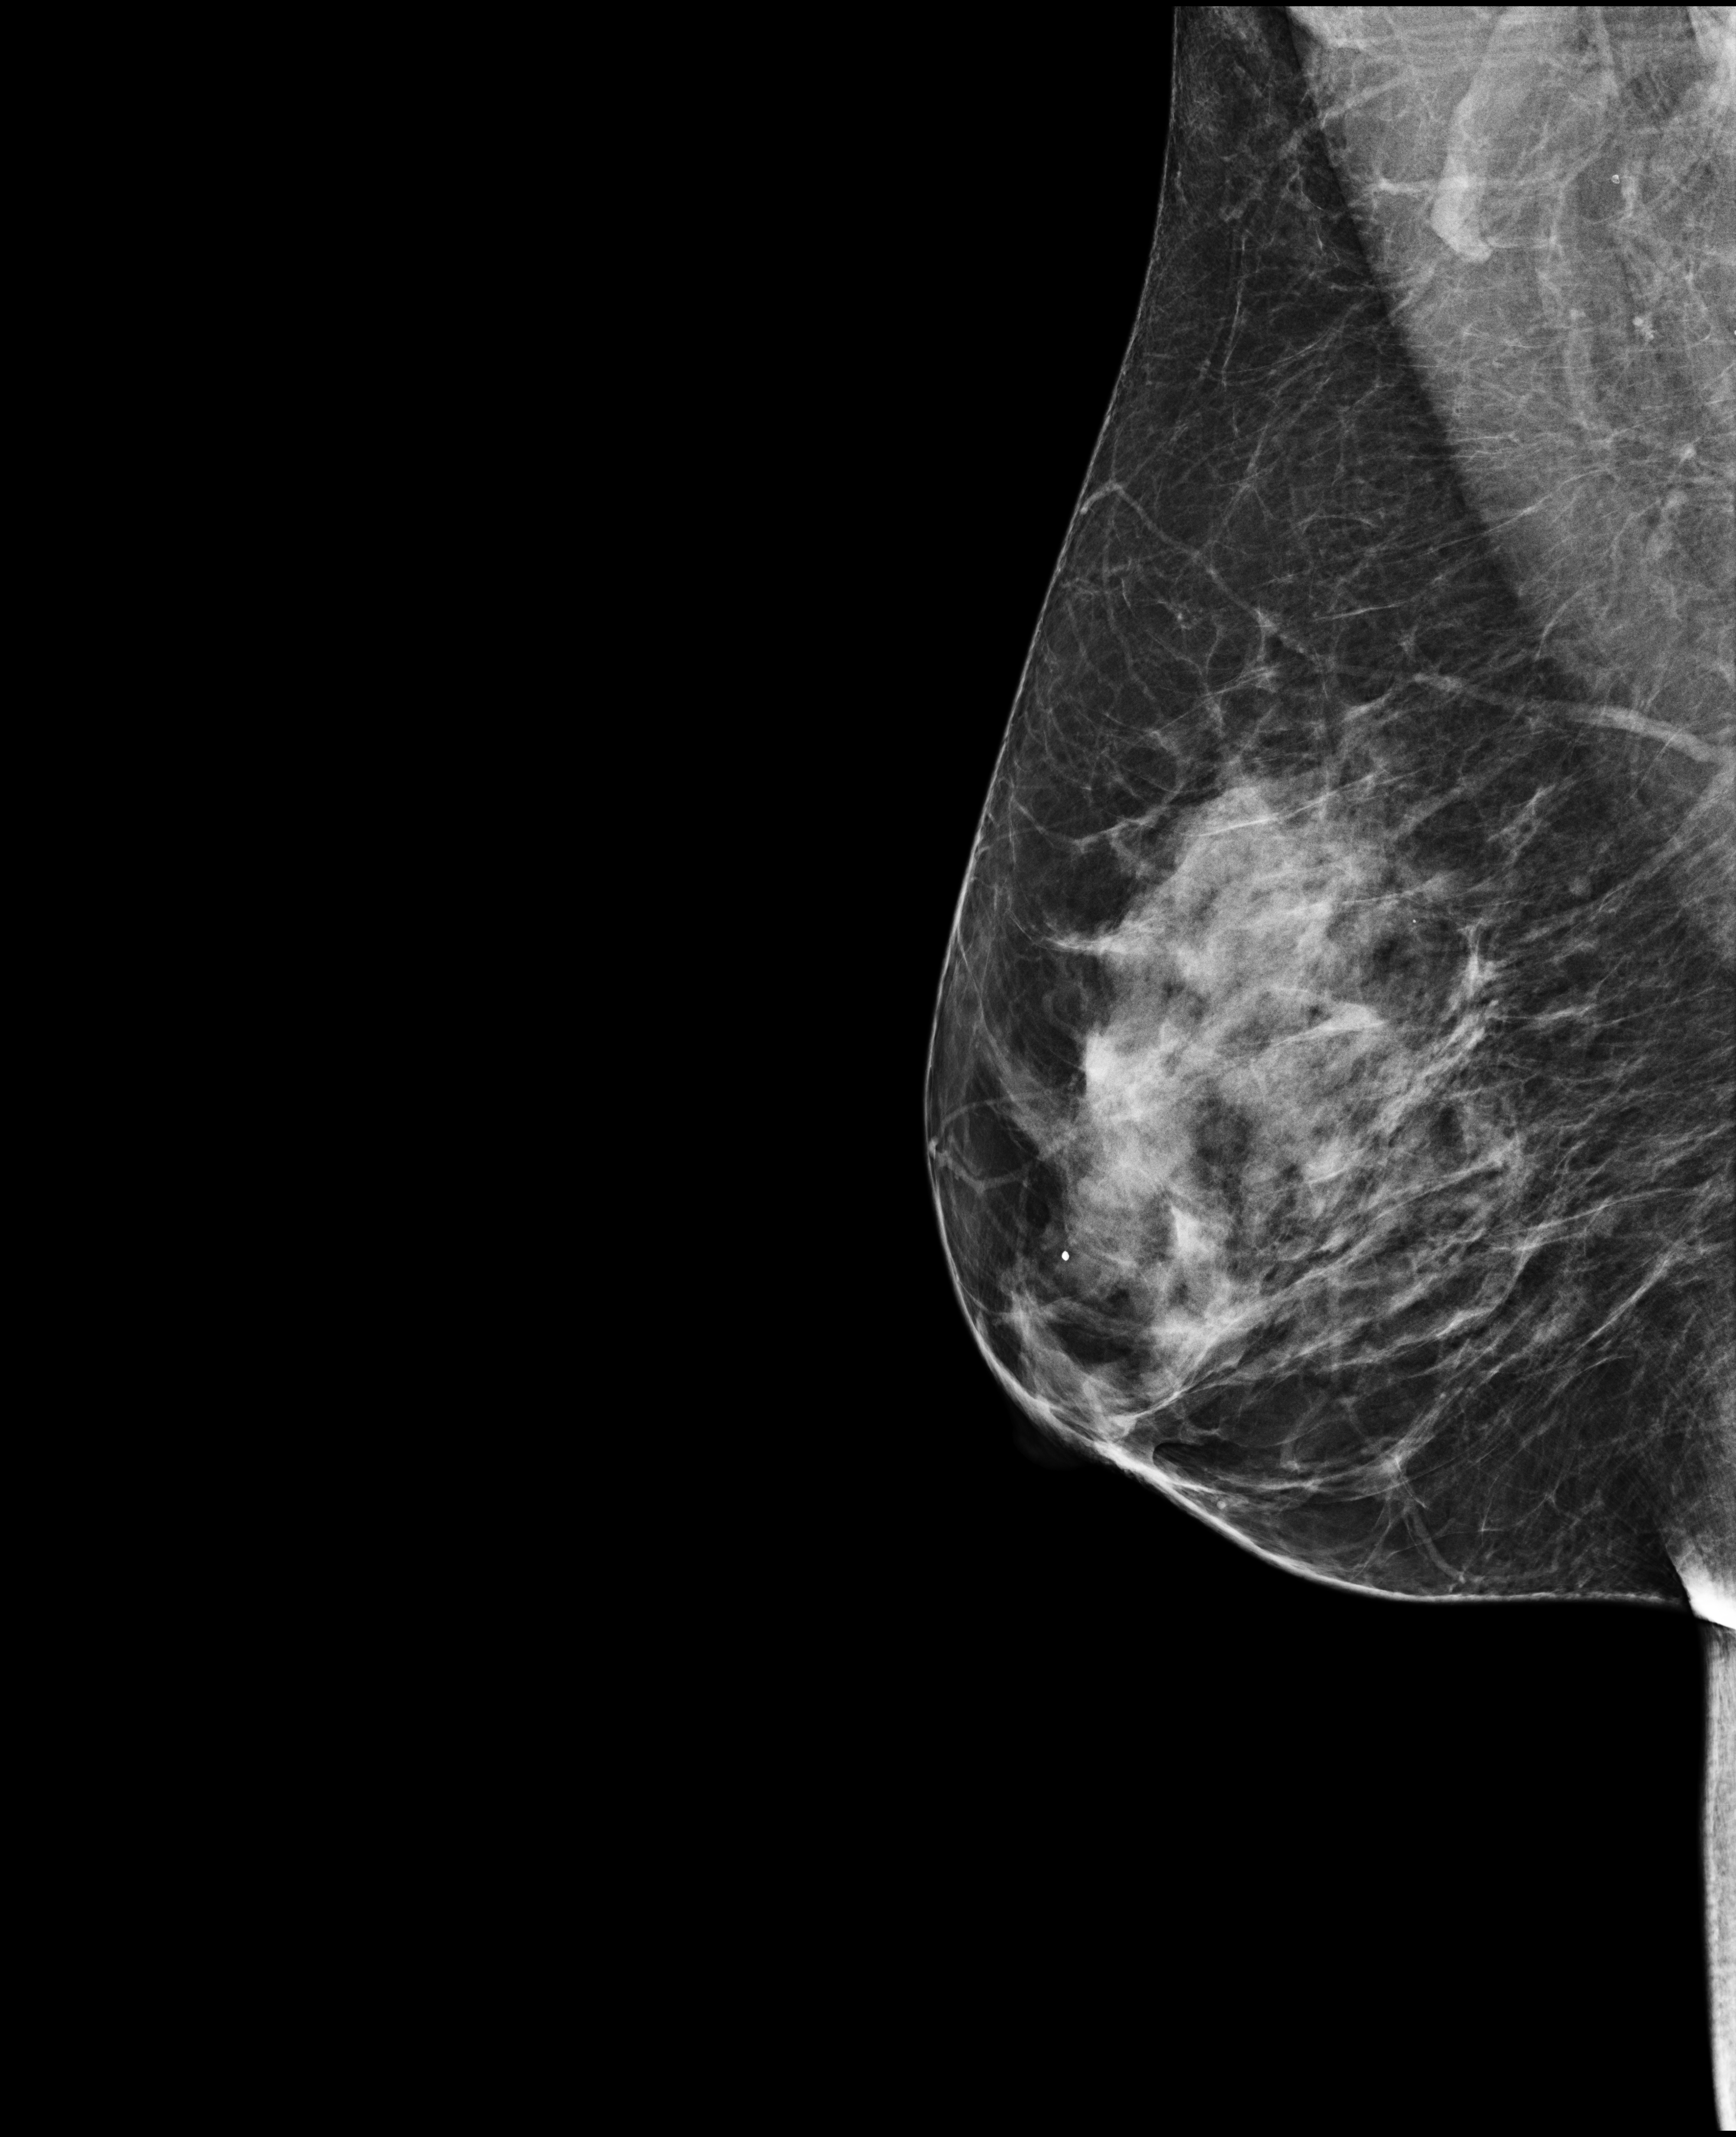
Full-field digital mammogram (FFDM), right breast, mediolateral oblique (MLO) view, screening examination, compressed breast thickness 61 mm, system: Selenia Dimensions. Patient: female, 48 years.
Final BI-RADS category for the screening round (tomosynthesis exam, both breasts): category 1.